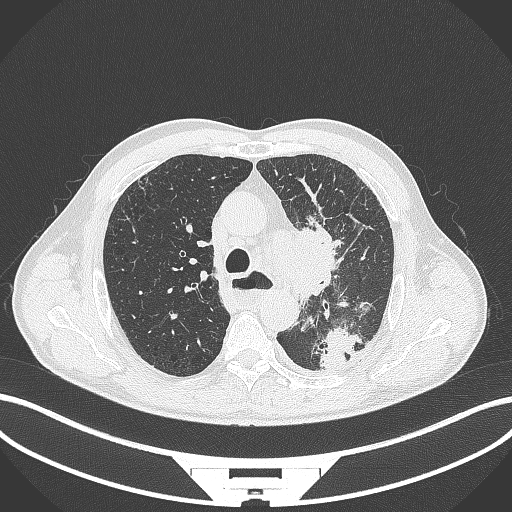
Chest CT, one axial slice. Position 269 of 411 along the scan axis. Reconstruction kernel B70f. 120 kVp. Lung window (W 1500 / L -600 HU). 1 mm slice thickness. 512 × 512 image matrix, field of view 400 × 400 mm. Patient: male, 57 years. Case-level facts recorded for this patient, not image findings: clinical TNM (as recorded): T2a N1 M0.
Annotated regions visible in this slice (rectangle marked by the reading radiologist):
- lung tumour (recorded histology: squamous cell carcinoma): bounding box <293,221,345,305> (left, top, right, bottom; pixels)